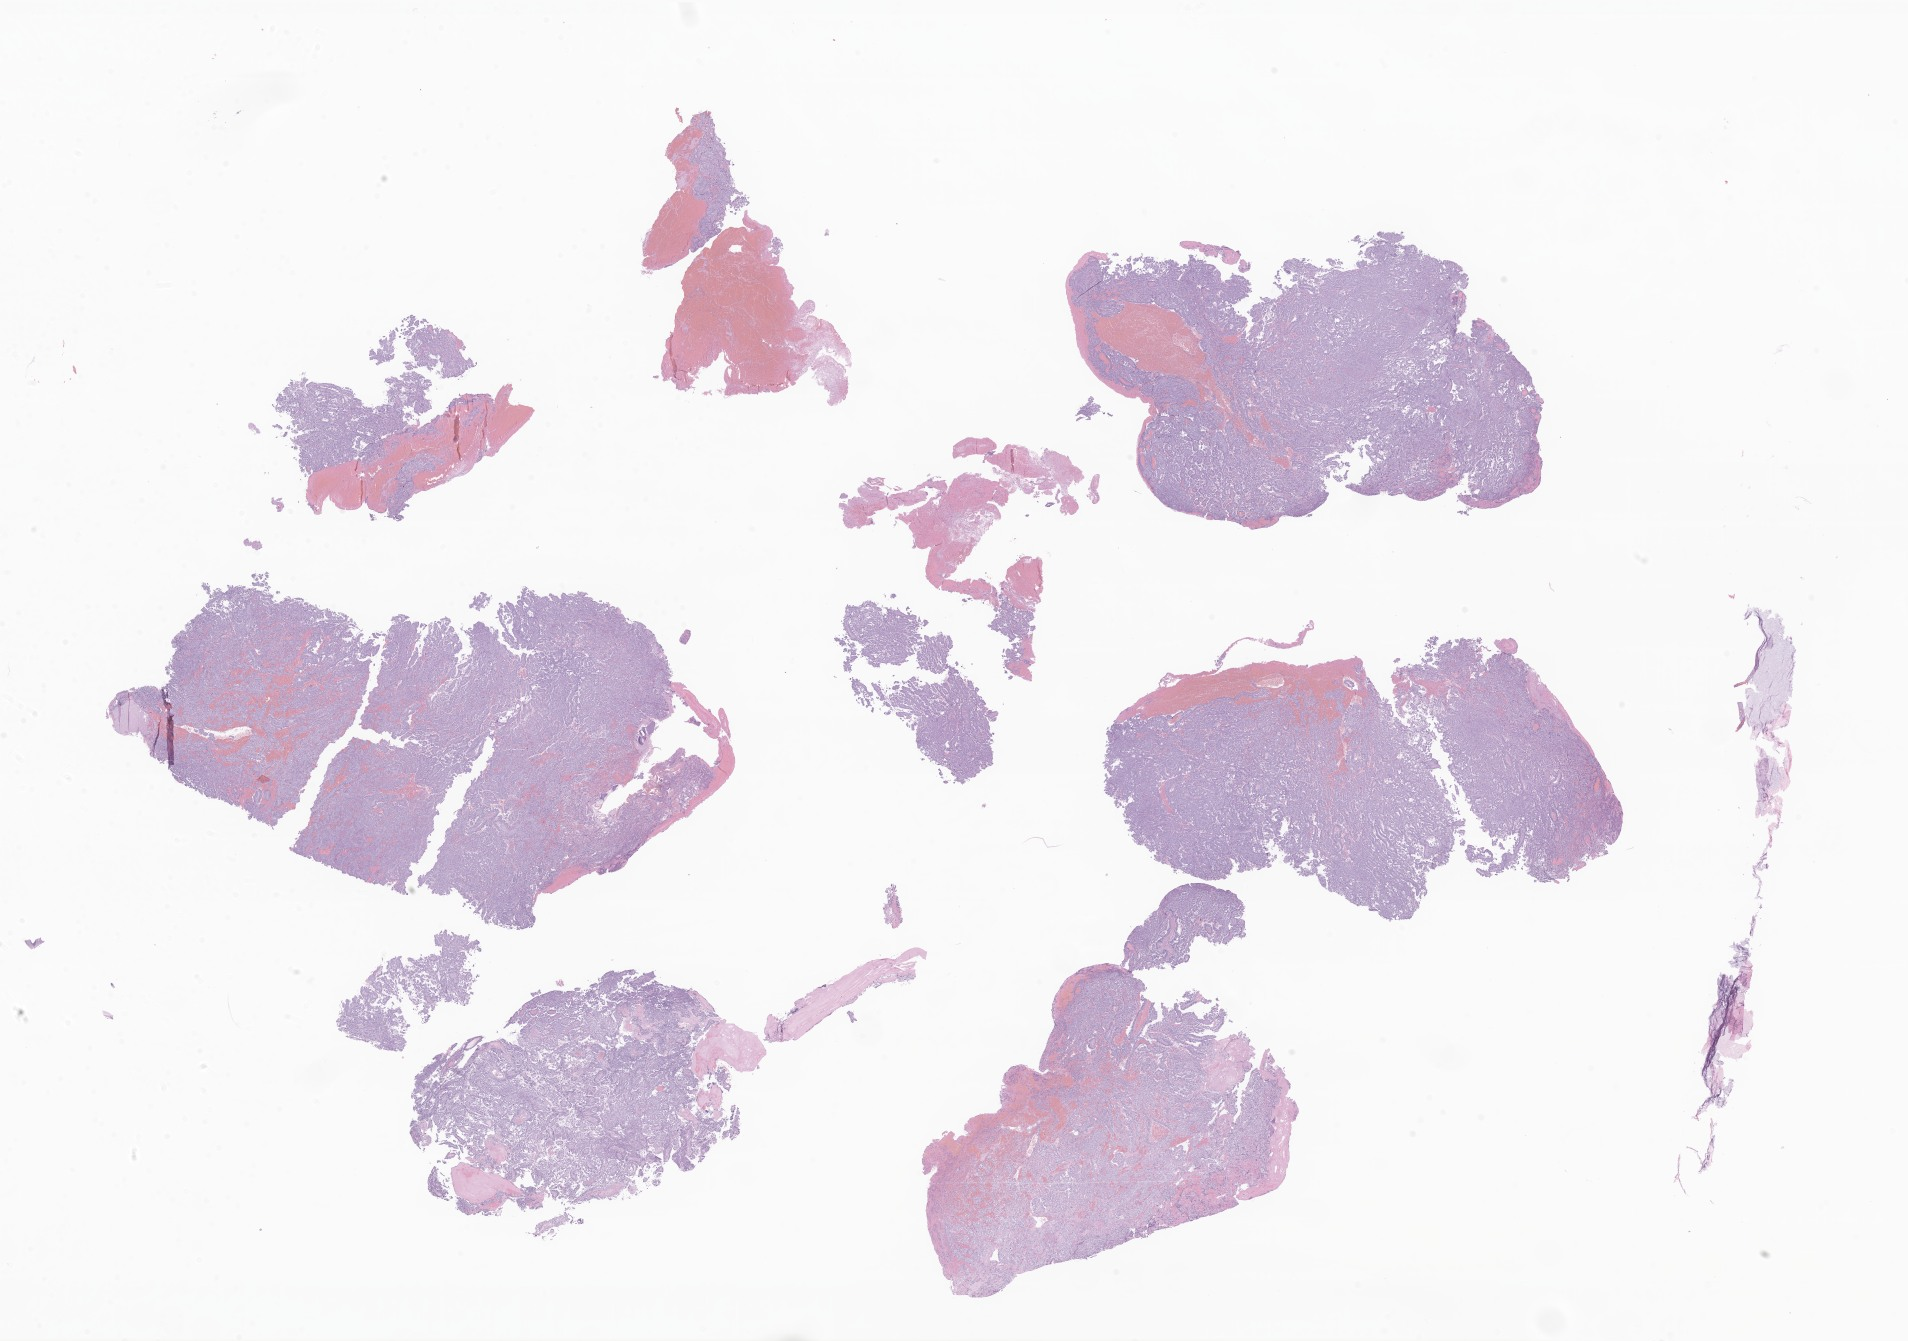
Whole-slide image, H&E stain of tumor tissue from the cerebral ventricle — shown as a low-resolution overview of the whole scanned area (about 32.2 x 22.6 mm); formalin-fixed, paraffin-embedded (FFPE) tissue. Male patient, age 39 months.
Recorded diagnosis: Choroid plexus carcinoma.